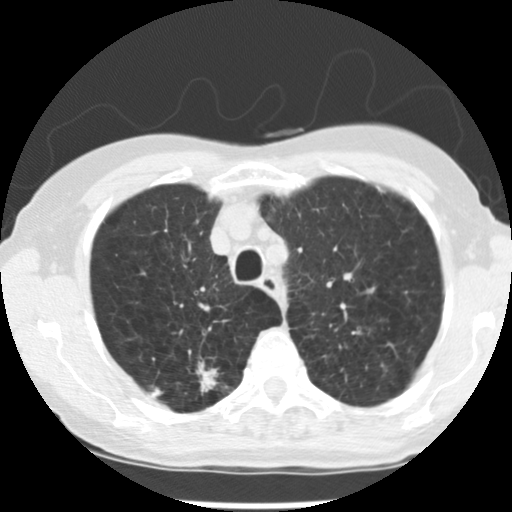
Axial slice from a low-dose chest CT screening exam, baseline screening round, lung window (W 1500 / L -600 HU), 2.5 mm slice thickness. Female, age 72 years at enrolment.
• Expert-annotated lung lesion, bounding box (x1, y1, x2, y2) in pixels: (183, 356, 237, 406).
• The screening reader recorded 3 non-calcified nodules or masses ≥4 mm on this exam (right upper lobe, left upper lobe, left lower lobe); which of them this box marks is not recorded.
• Later outcome: lung cancer diagnosed 50 days after this screen — adenocarcinoma, NOS, right upper lobe, moderately differentiated (G2), stage IB (AJCC 6th edition), 22 mm at pathology.